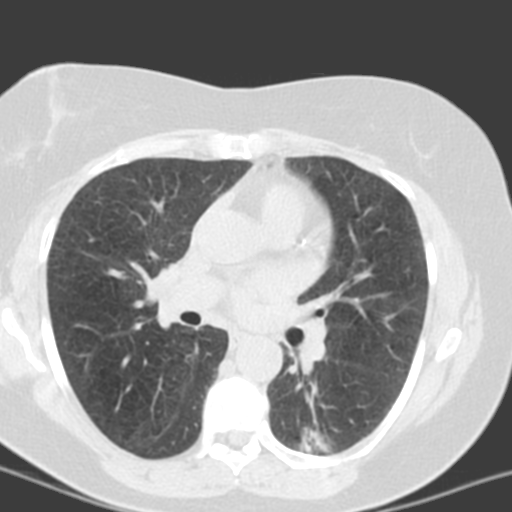
Low-dose screening chest CT, axial slice; third annual screen; lung window (W 1500 / L -600 HU); 3.2 mm slice thickness; slice 61 of 150 in the series. Female participant, aged 55 years at enrolment. Current smoker at enrolment.
Expert reader's lesion annotation, bounding box <286,411,364,464> (left, top, right, bottom; pixels). The screening reader recorded 6 non-calcified nodules or masses ≥4 mm on this exam (left lower lobe, left lower lobe, left upper lobe, lingula, lingula, right middle lobe); which of them this box marks is not recorded. Lung cancer was diagnosed 357 days after this screen: adenocarcinoma with mixed subtypes, left lower lobe, poorly differentiated (G3), stage IA (AJCC 6th edition), 21 mm at pathology.